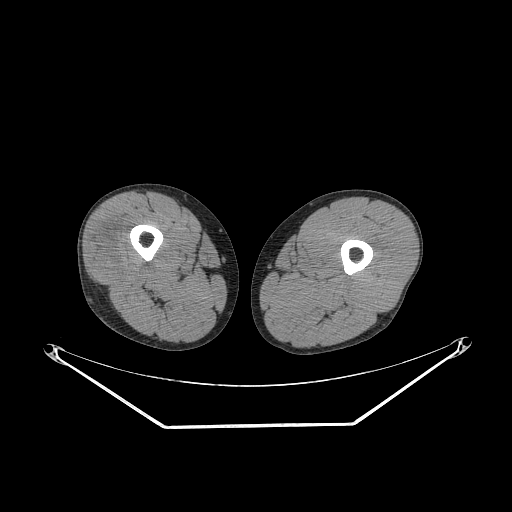
CT of an extremity soft-tissue mass (from a PET/CT study), one axial slice. Slice 226 of 267 in the series (ordered by position). Reconstruction kernel STANDARD. Soft-tissue window (W 400 / L 40 HU). 3.75 mm slice thickness. 512 × 512 image matrix, field of view 500 × 500 mm. Male patient. From the clinical record (not read from this slice): histological type: poorly differentiated synovial sarcoma; grade: high; site of the primary tumour: right buttock.
Outlined on this slice (expert contour drawn on MRI and transferred to this co-registered scan by the dataset authors):
- gross tumour volume including surrounding oedema: bounding box [x1, y1, x2, y2] px = [91, 231, 138, 280]